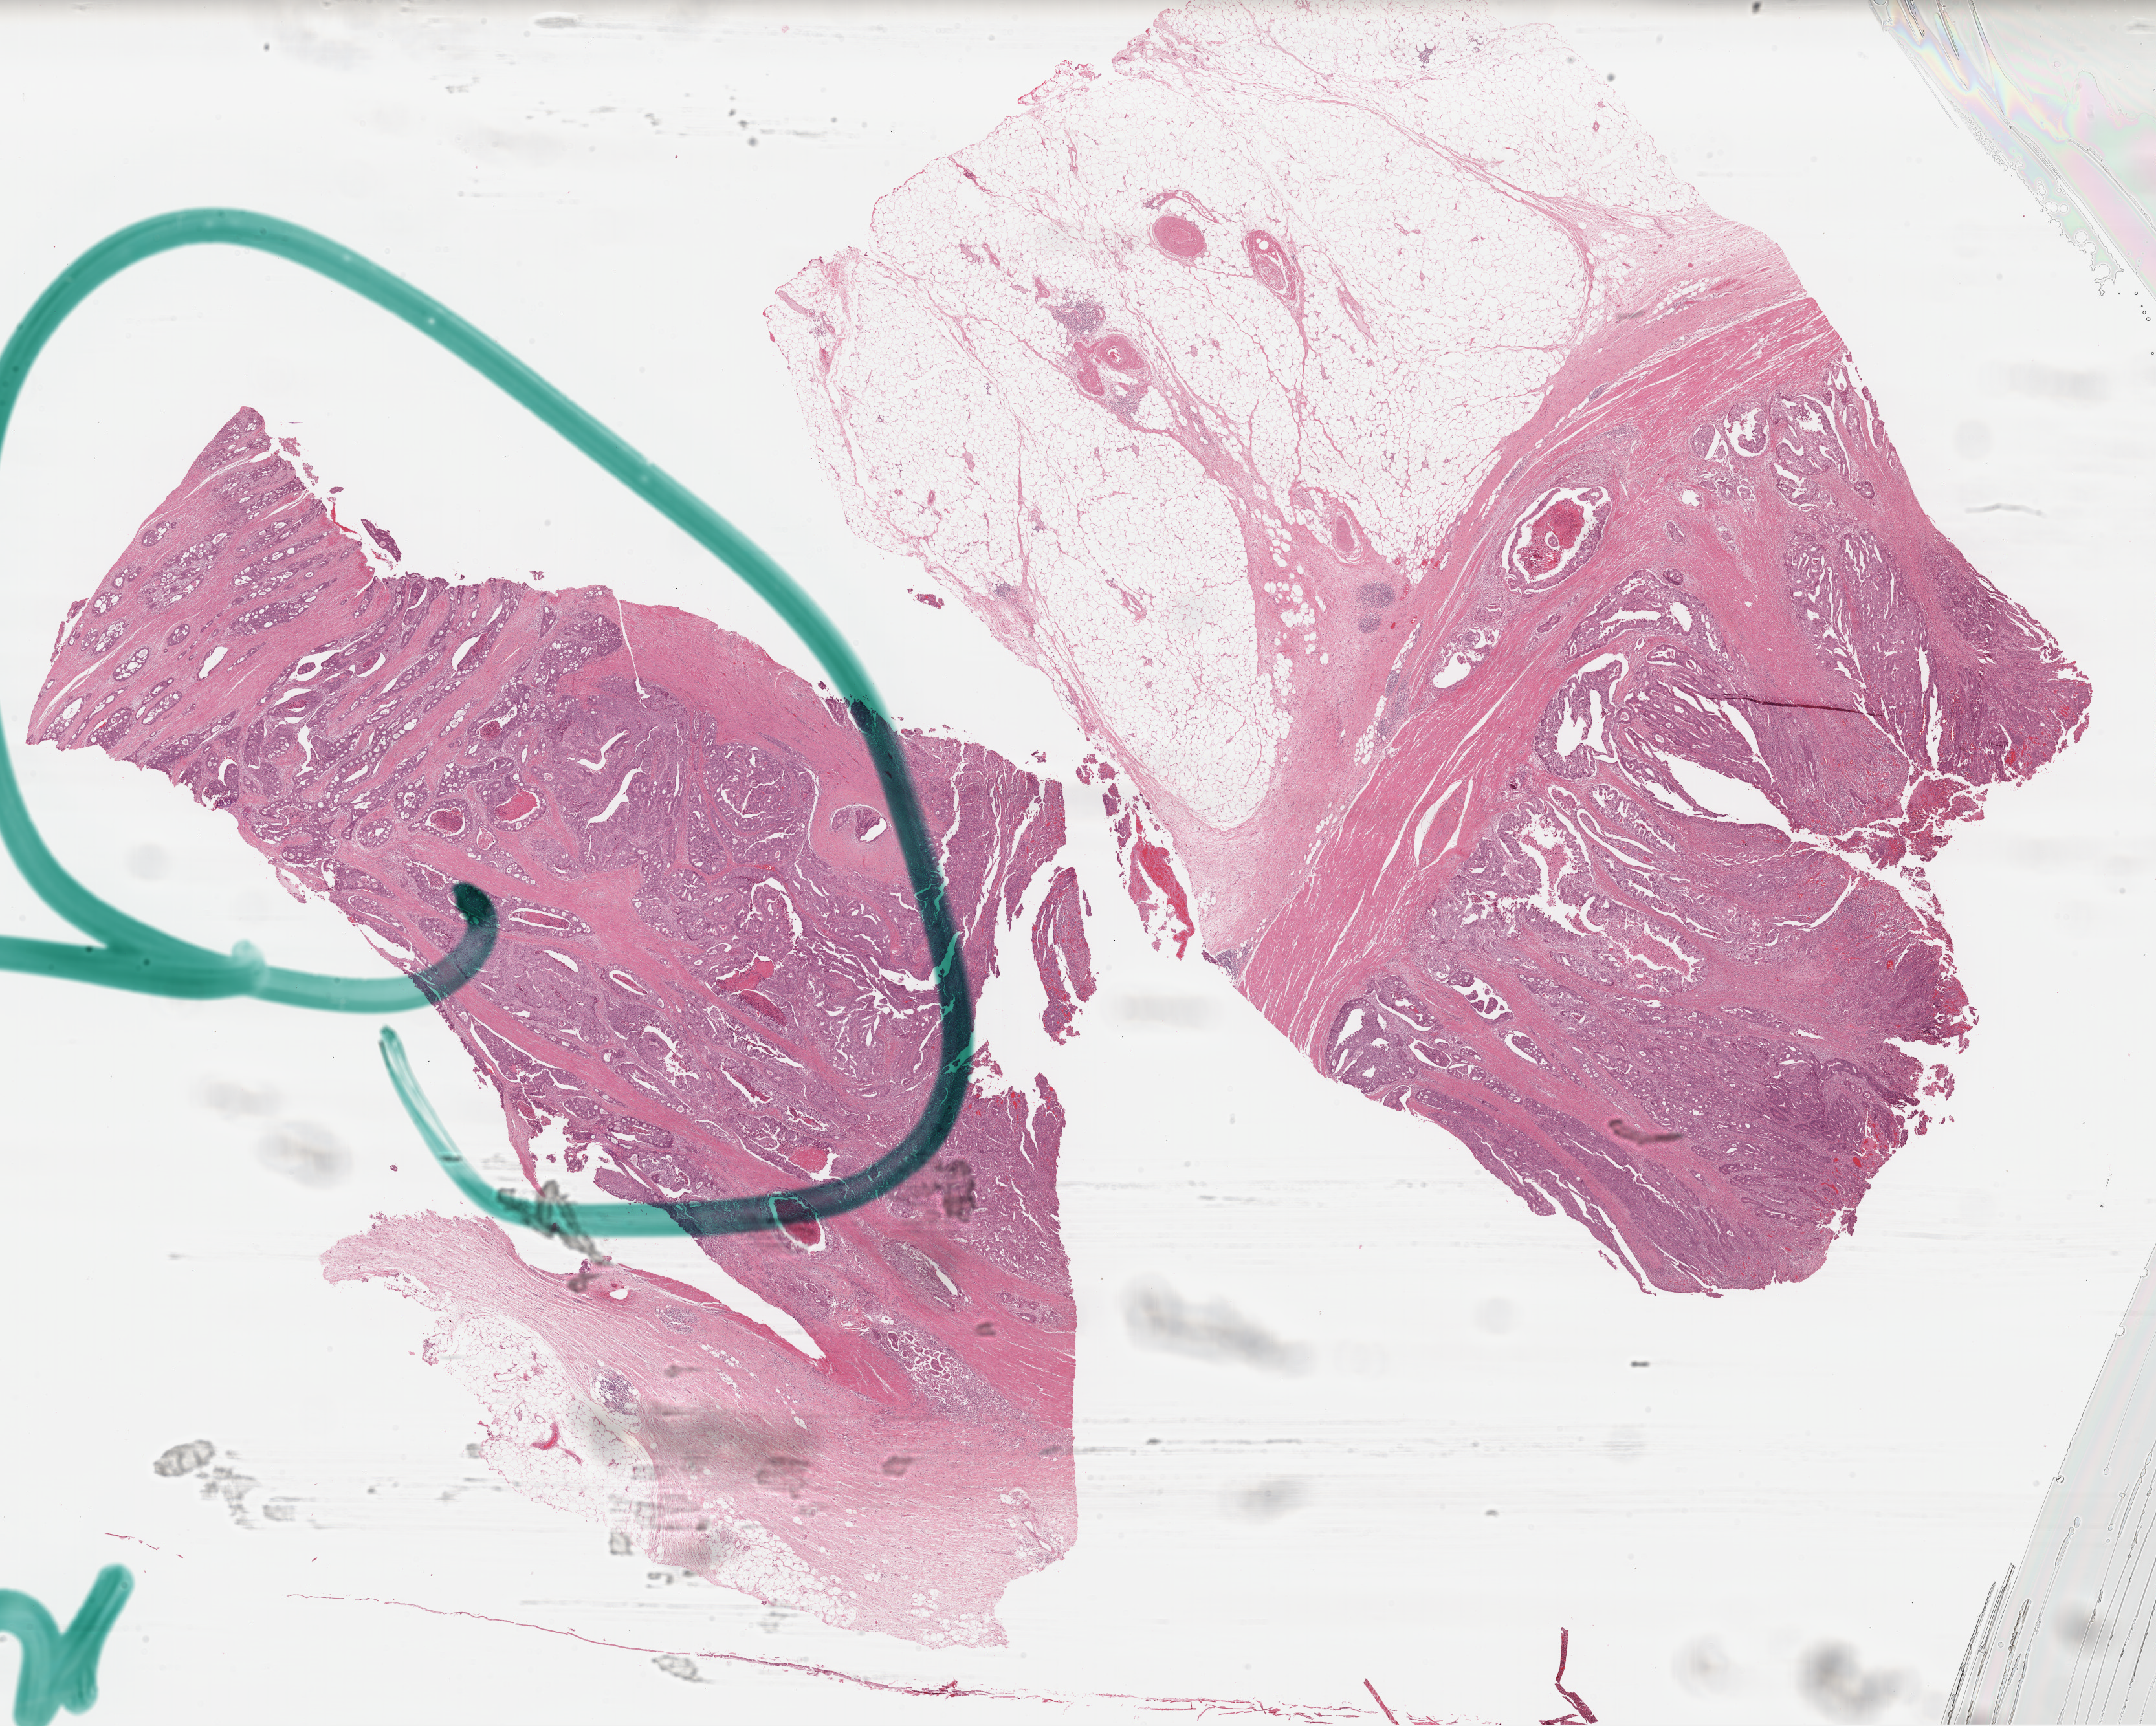
Digitized Hematoxylin and eosin (H&E) stained tissue section (whole slide) — a low-resolution overview of the entire scanned area, about 26.3 x 21.1 mm. Formalin-fixed paraffin-embedded (FFPE) diagnostic section. Primary tumour sample from the colon. Patient: female, age at initial diagnosis 68 years.
Diagnosis: Adenocarcinoma, NOS (sigmoid colon).